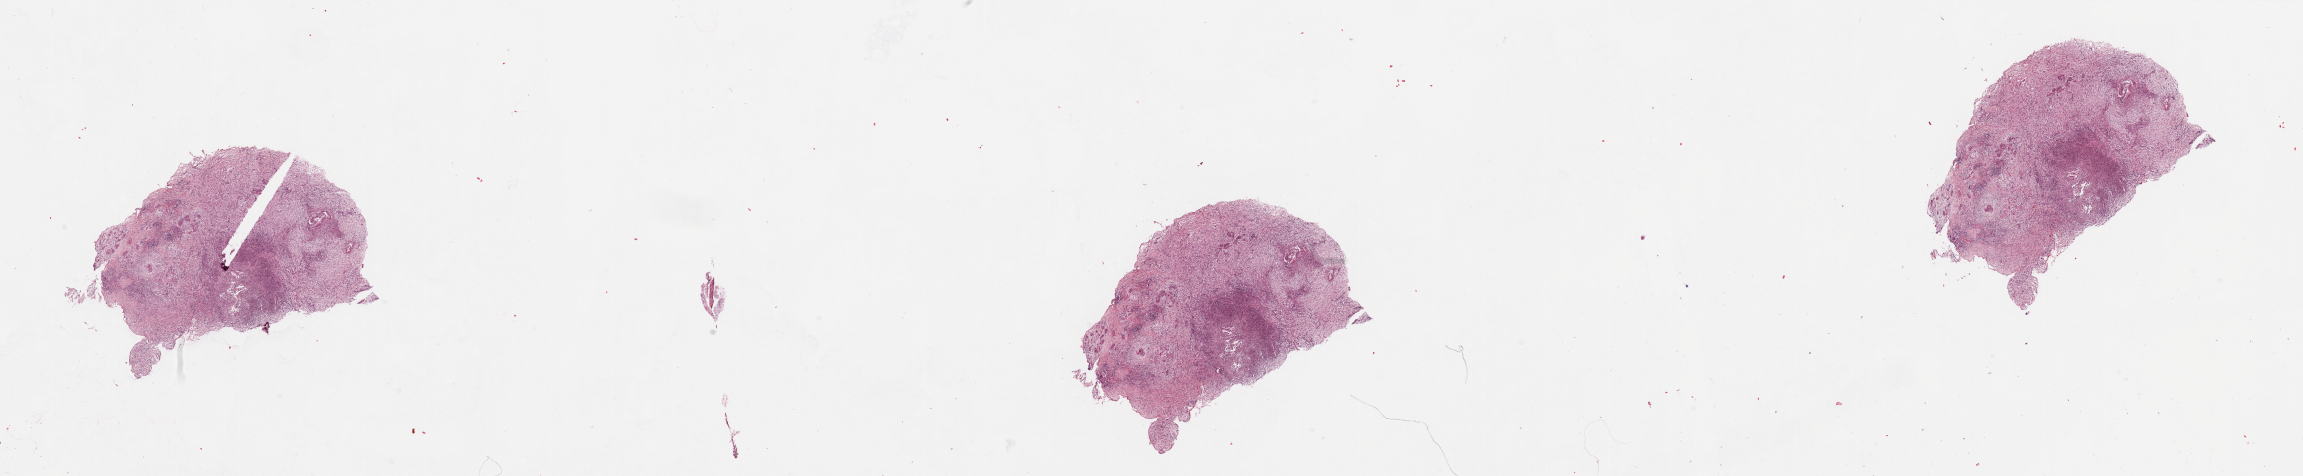
Digitized Hematoxylin and eosin (H&E) stained tissue section (whole slide), whole scanned area (about 36.4 x 7.5 mm, from a 20x scan) shown as a low-resolution overview. Pancreas, tumour tissue. Patient: male, age 66 years.
Primary tumour site (as recorded): head. Patient diagnosis (cohort enrolment): ductal adenocarcinoma (pancreas).